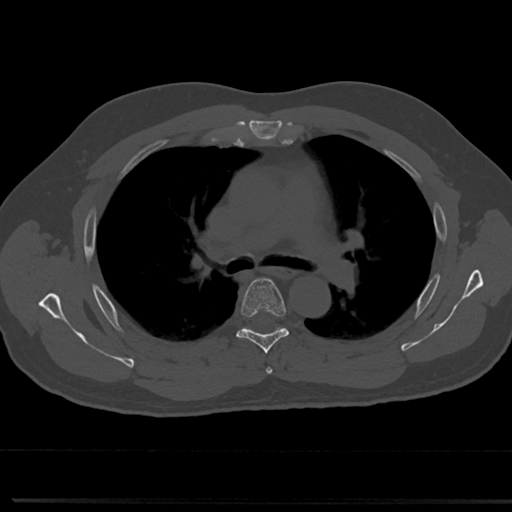
CT including the spine, one axial slice; slice 496 of 817 in the series (ordered by position); reconstruction kernel Br40s/3; bone window (W 1800 / L 400 HU); 0.5 mm slice thickness; 512 × 512 image matrix, field of view 355 × 355 mm. Patient: male, 61 years. From the clinical record (not read from this slice): primary cancer: prostate.
Outlined on this slice (semi-automatic segmentation, software-assisted and operator-edited):
- T4 vertebra: bounding box <264,357,273,374> (left, top, right, bottom; pixels)
- T5 vertebra: <218,277,306,350>